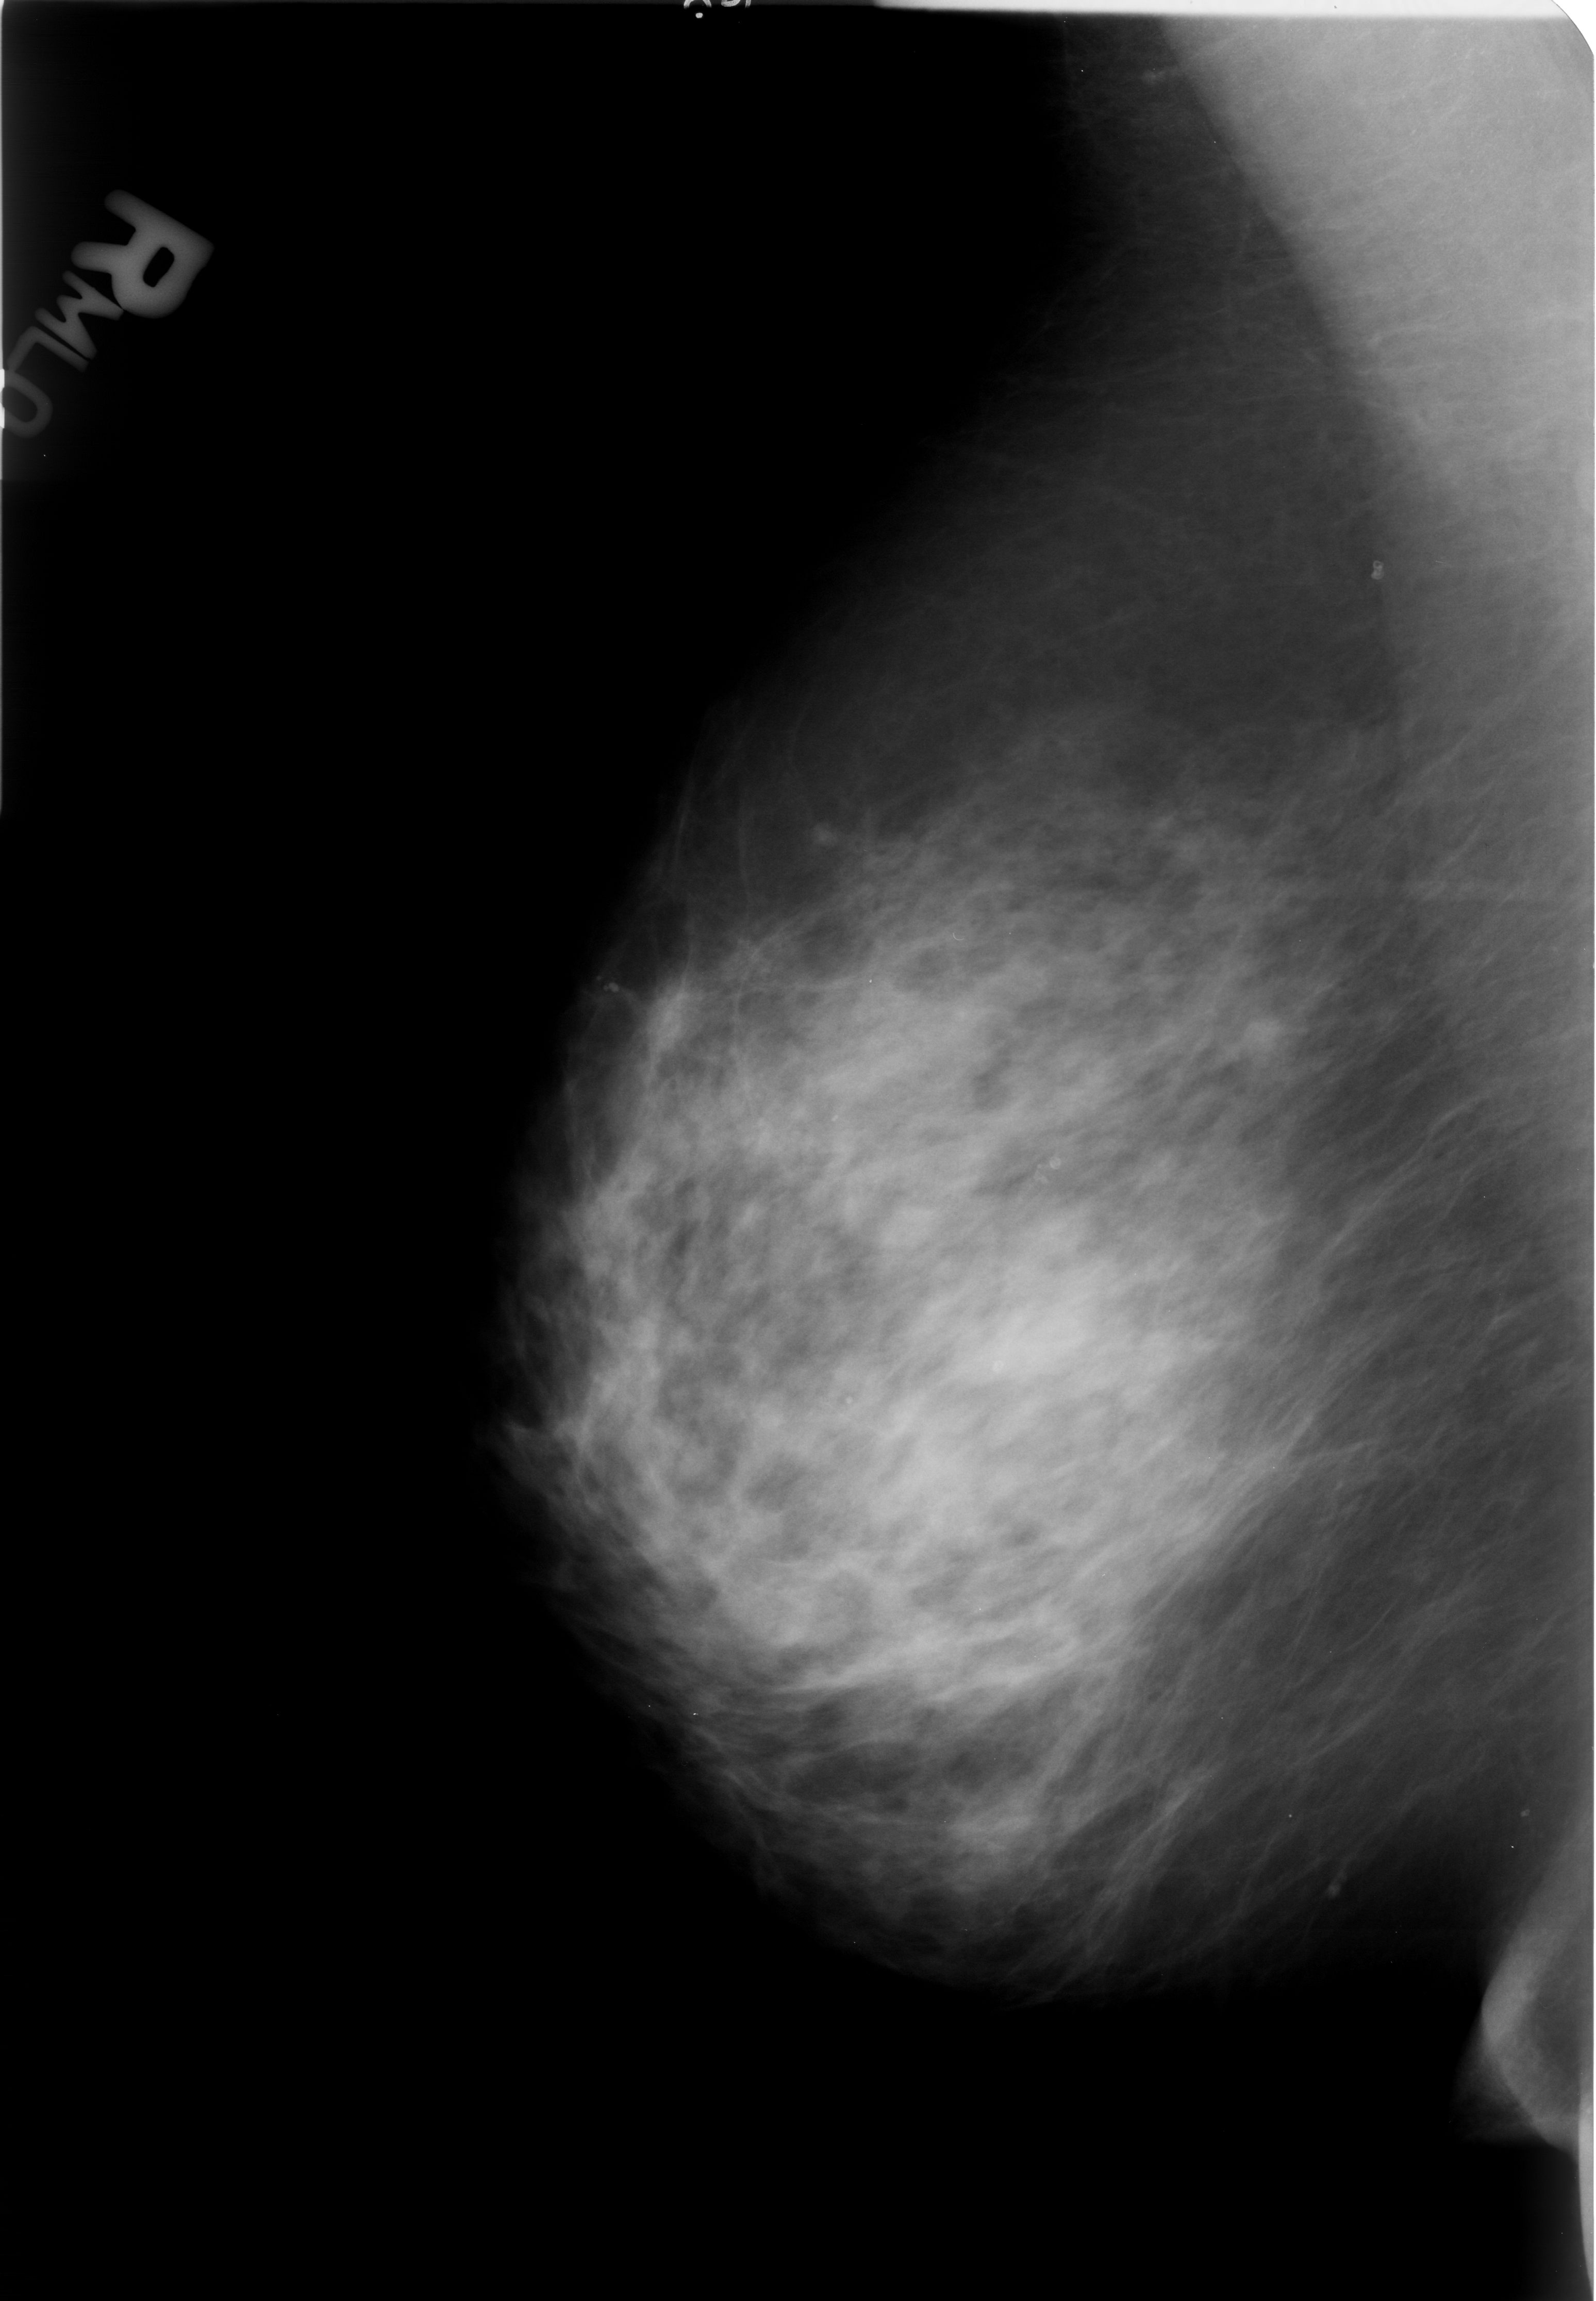
Digitized screen-film mammogram; right breast; MLO view; BI-RADS breast density category 3 (scale 1–4); 1596 × 2301 image matrix.
Marked abnormalities (boxes around the expert regions of interest):
- Finding 1 of 3: calcifications, morphology lucent centered; BI-RADS assessment category 2; subtlety rating 3 on a 1 (subtle) to 5 (obvious) scale; benign; no additional work-up was recommended (outcome (as recorded, no biopsy): benign without callback): box from (x=828, y=1385) to (x=867, y=1432) px
- Finding 2 of 3: calcifications, morphology lucent centered; BI-RADS assessment category 2; benign; no additional work-up was recommended (outcome (as recorded, no biopsy): benign without callback): (x=981, y=1348)–(x=1016, y=1399)
- Finding 3 of 3: calcifications, morphology lucent centered; BI-RADS assessment category 2; outcome (as recorded, no biopsy): benign without callback (not worked up further): (x=1031, y=1142)–(x=1077, y=1180)